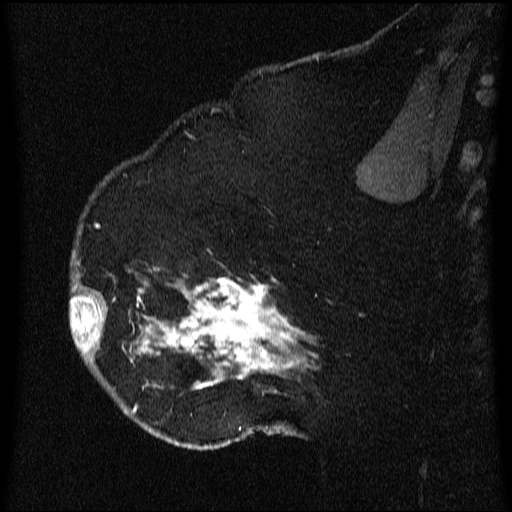
Breast MRI (dynamic contrast-enhanced), one sagittal slice. Position 43 of 64 along the scan axis. Dynamic contrast-enhanced series, image 2 of 3 at this slice position (ordered by acquisition). 1.5 T. TE 4.2 ms, TR 9.1 ms. 2.2 mm slice thickness. 512 × 512 image matrix, field of view 180 × 180 mm. Female patient, age 52 years.
Outlined on this slice (semi-automatically segmented with operator editing):
- analysis volume of interest (the breast-tissue region the enhancement analysis was run in; not a lesion): box from (x=71, y=203) to (x=322, y=438) px
- tumour enhancement mask (voxels above the 70 % enhancement threshold inside the analysis volume of interest): (x=71, y=225)–(x=319, y=435)